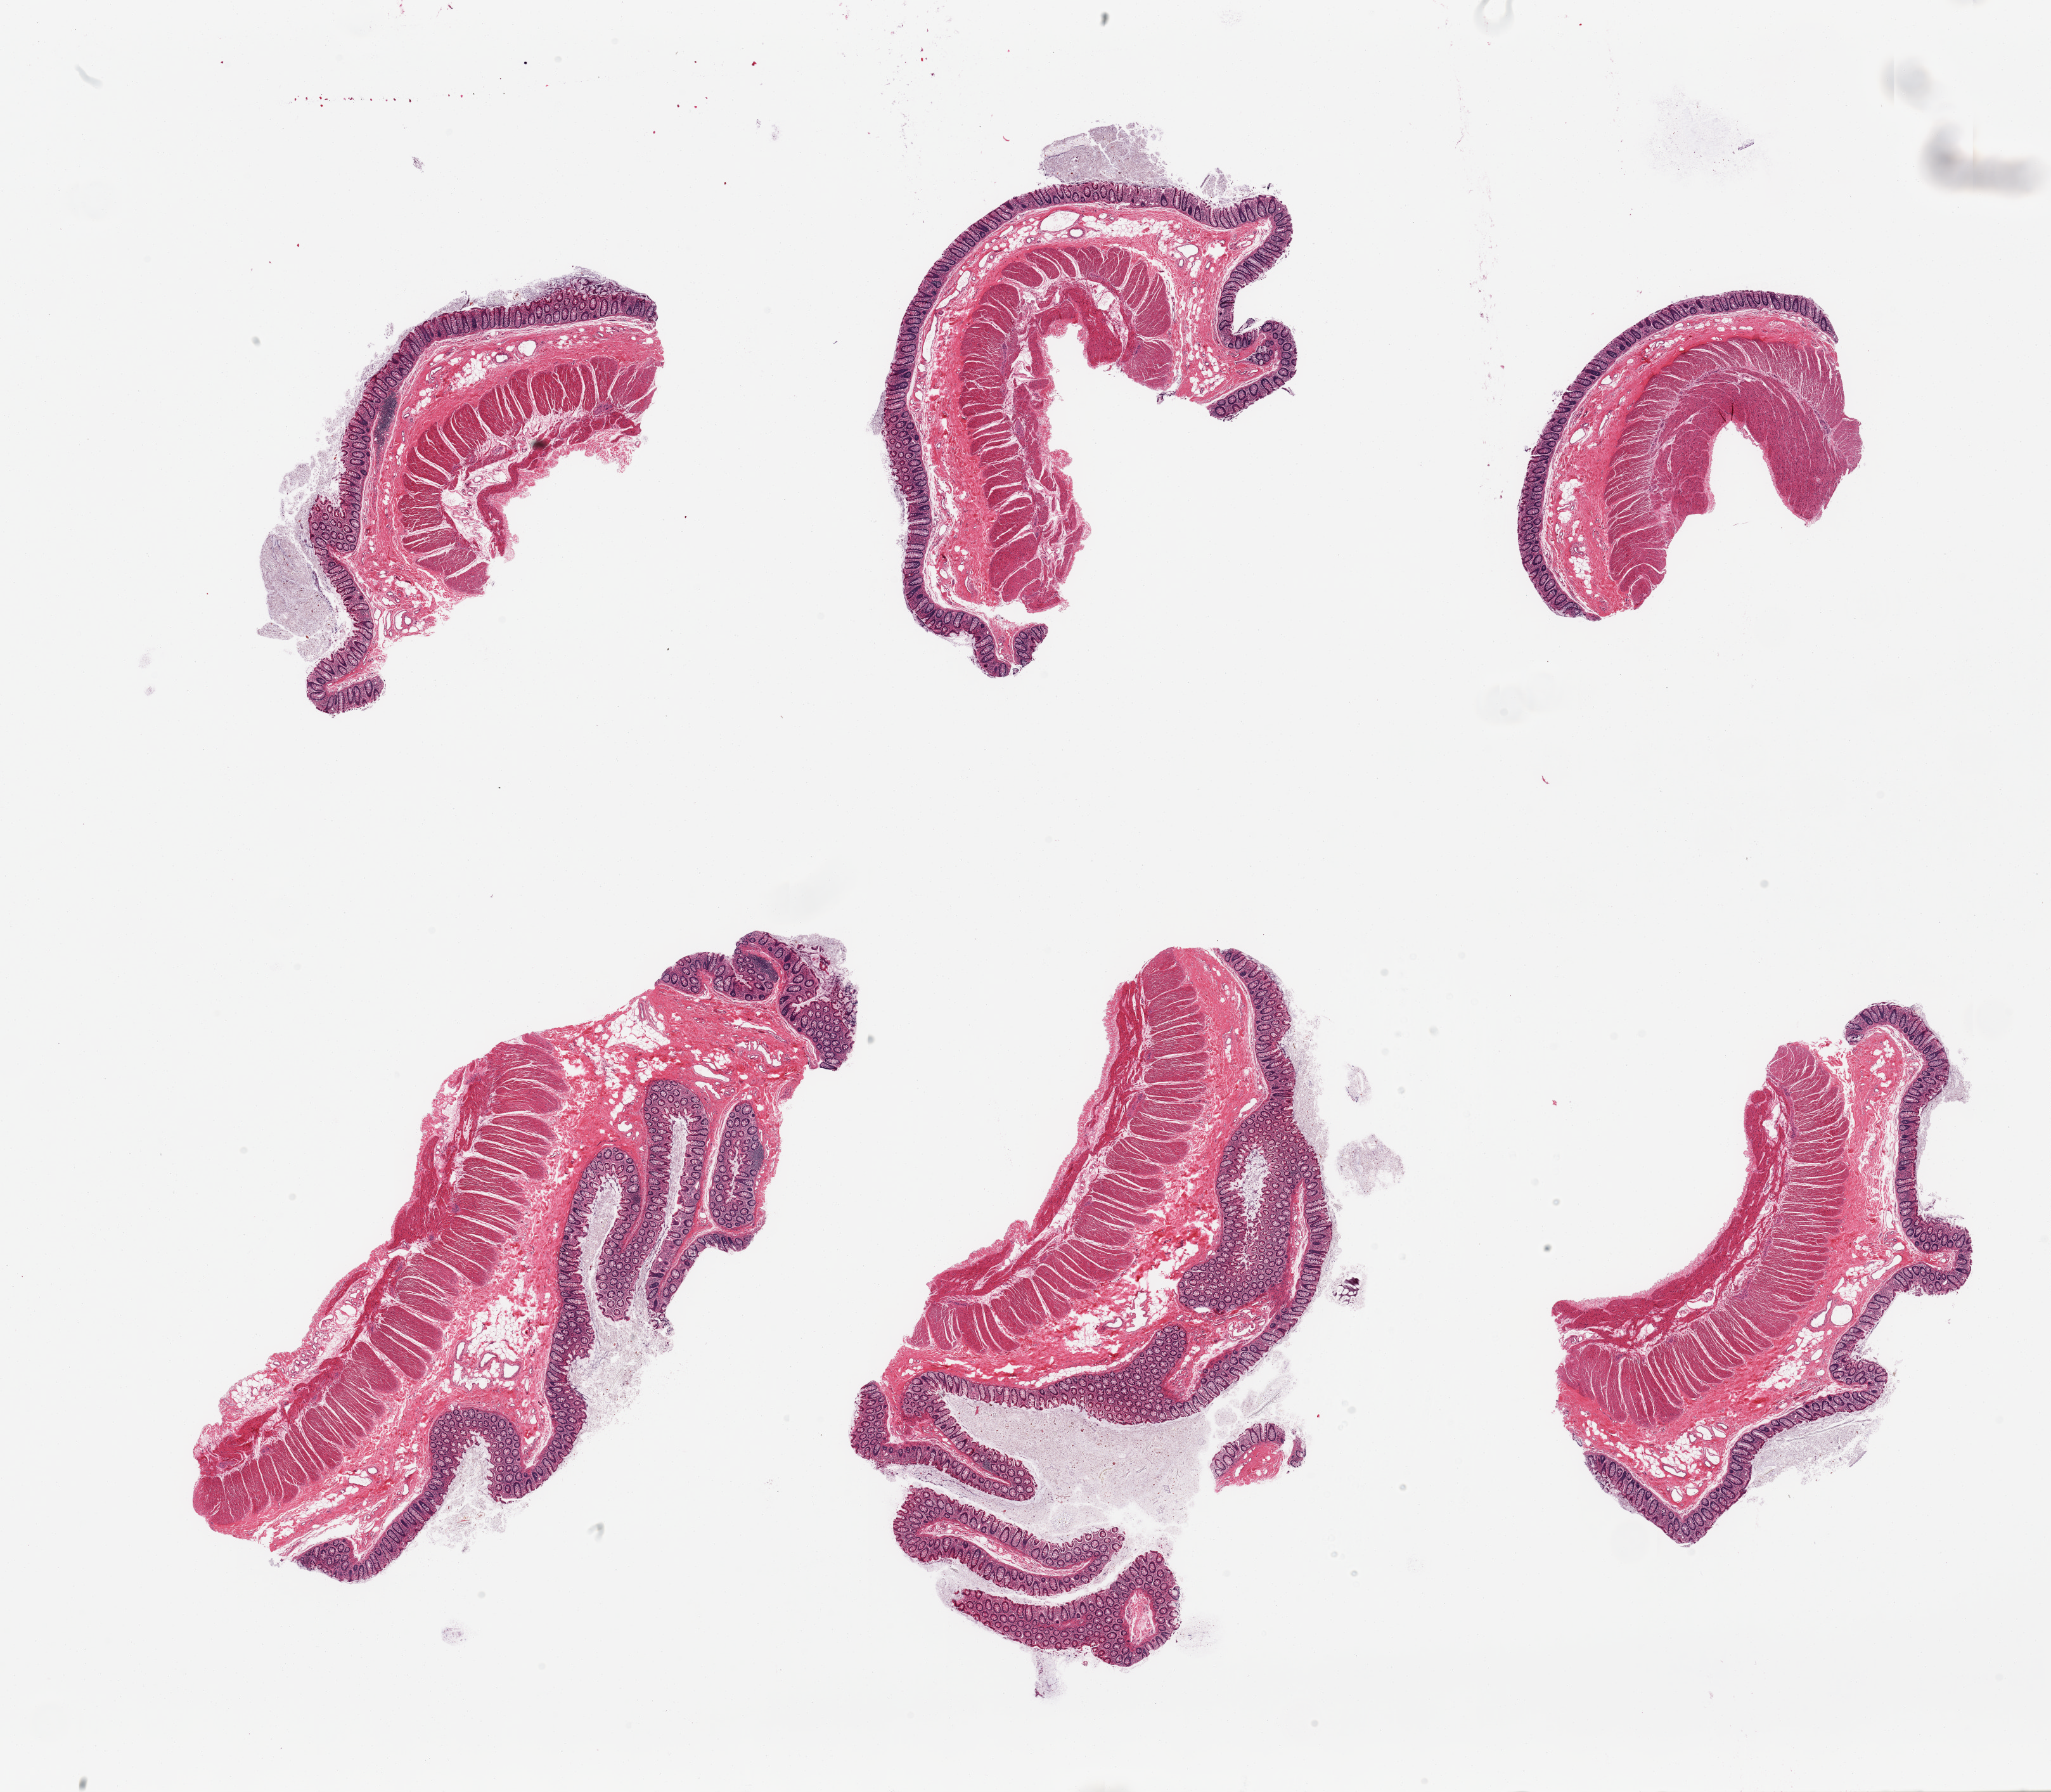
Whole-slide image, hematoxylin and eosin (H&E) stain — low-resolution overview of the scanned area, about 25.6 x 22.4 mm (acquisition: 20x scan), PAXgene-fixed, paraffin-embedded tissue, target tissue: transverse colon, tissue donor sample.
Pathologist's review note for this sample: 6 pieces; full thickness sections.